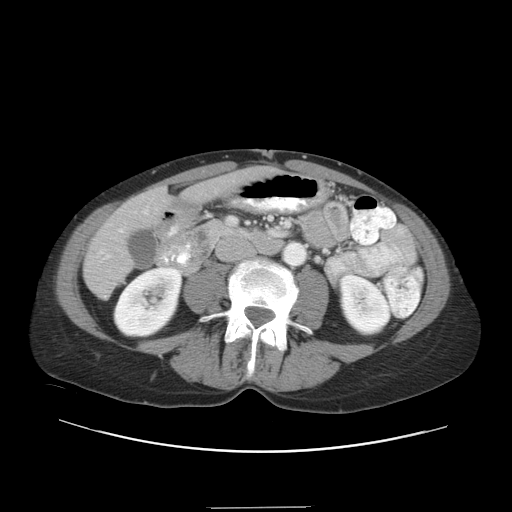
Contrast-enhanced abdominal CT, one axial slice. Slice 8 of 38 in the series (ordered by position). Reconstruction kernel STANDARD. 120 kVp. Intravenous contrast given. Soft-tissue window (W 400 / L 40 HU). 512 × 512 image matrix. Female patient, age 64 years. Case-level facts recorded for this patient, not image findings: diagnosis: colorectal cancer liver metastases, imaged before liver resection; multiple liver metastases: no; largest metastasis: 3.8 cm.
Outlined on this slice (manually delineated by an expert):
- hepatic veins: bounding box [x1, y1, x2, y2] px = [119, 210, 148, 233]
- liver: [85, 172, 264, 296]
- planned liver remnant (the part of the liver to remain after resection): [188, 172, 263, 198]
- portal vein (with intrahepatic branches): [107, 255, 110, 257]